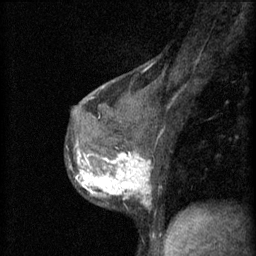
Breast MRI (dynamic contrast-enhanced), one sagittal slice. Position 34 of 60 along the scan axis. 3 images stored at this slice position (order not interpretable as contrast timing). 1.5 T. TE 4.2 ms, TR 11 ms. 2 mm slice thickness. 256 × 256 image matrix, field of view 180 × 180 mm. Female patient, age 37 years.
Structures marked on this image (semi-automatically segmented with operator editing):
- analysis volume of interest (the breast-tissue region the enhancement analysis was run in; not a lesion): bounding box (x1, y1, x2, y2) in pixels: (66, 138, 154, 207)
- tumour enhancement mask (voxels above the 70 % enhancement threshold inside the analysis volume of interest): (70, 144, 151, 201)